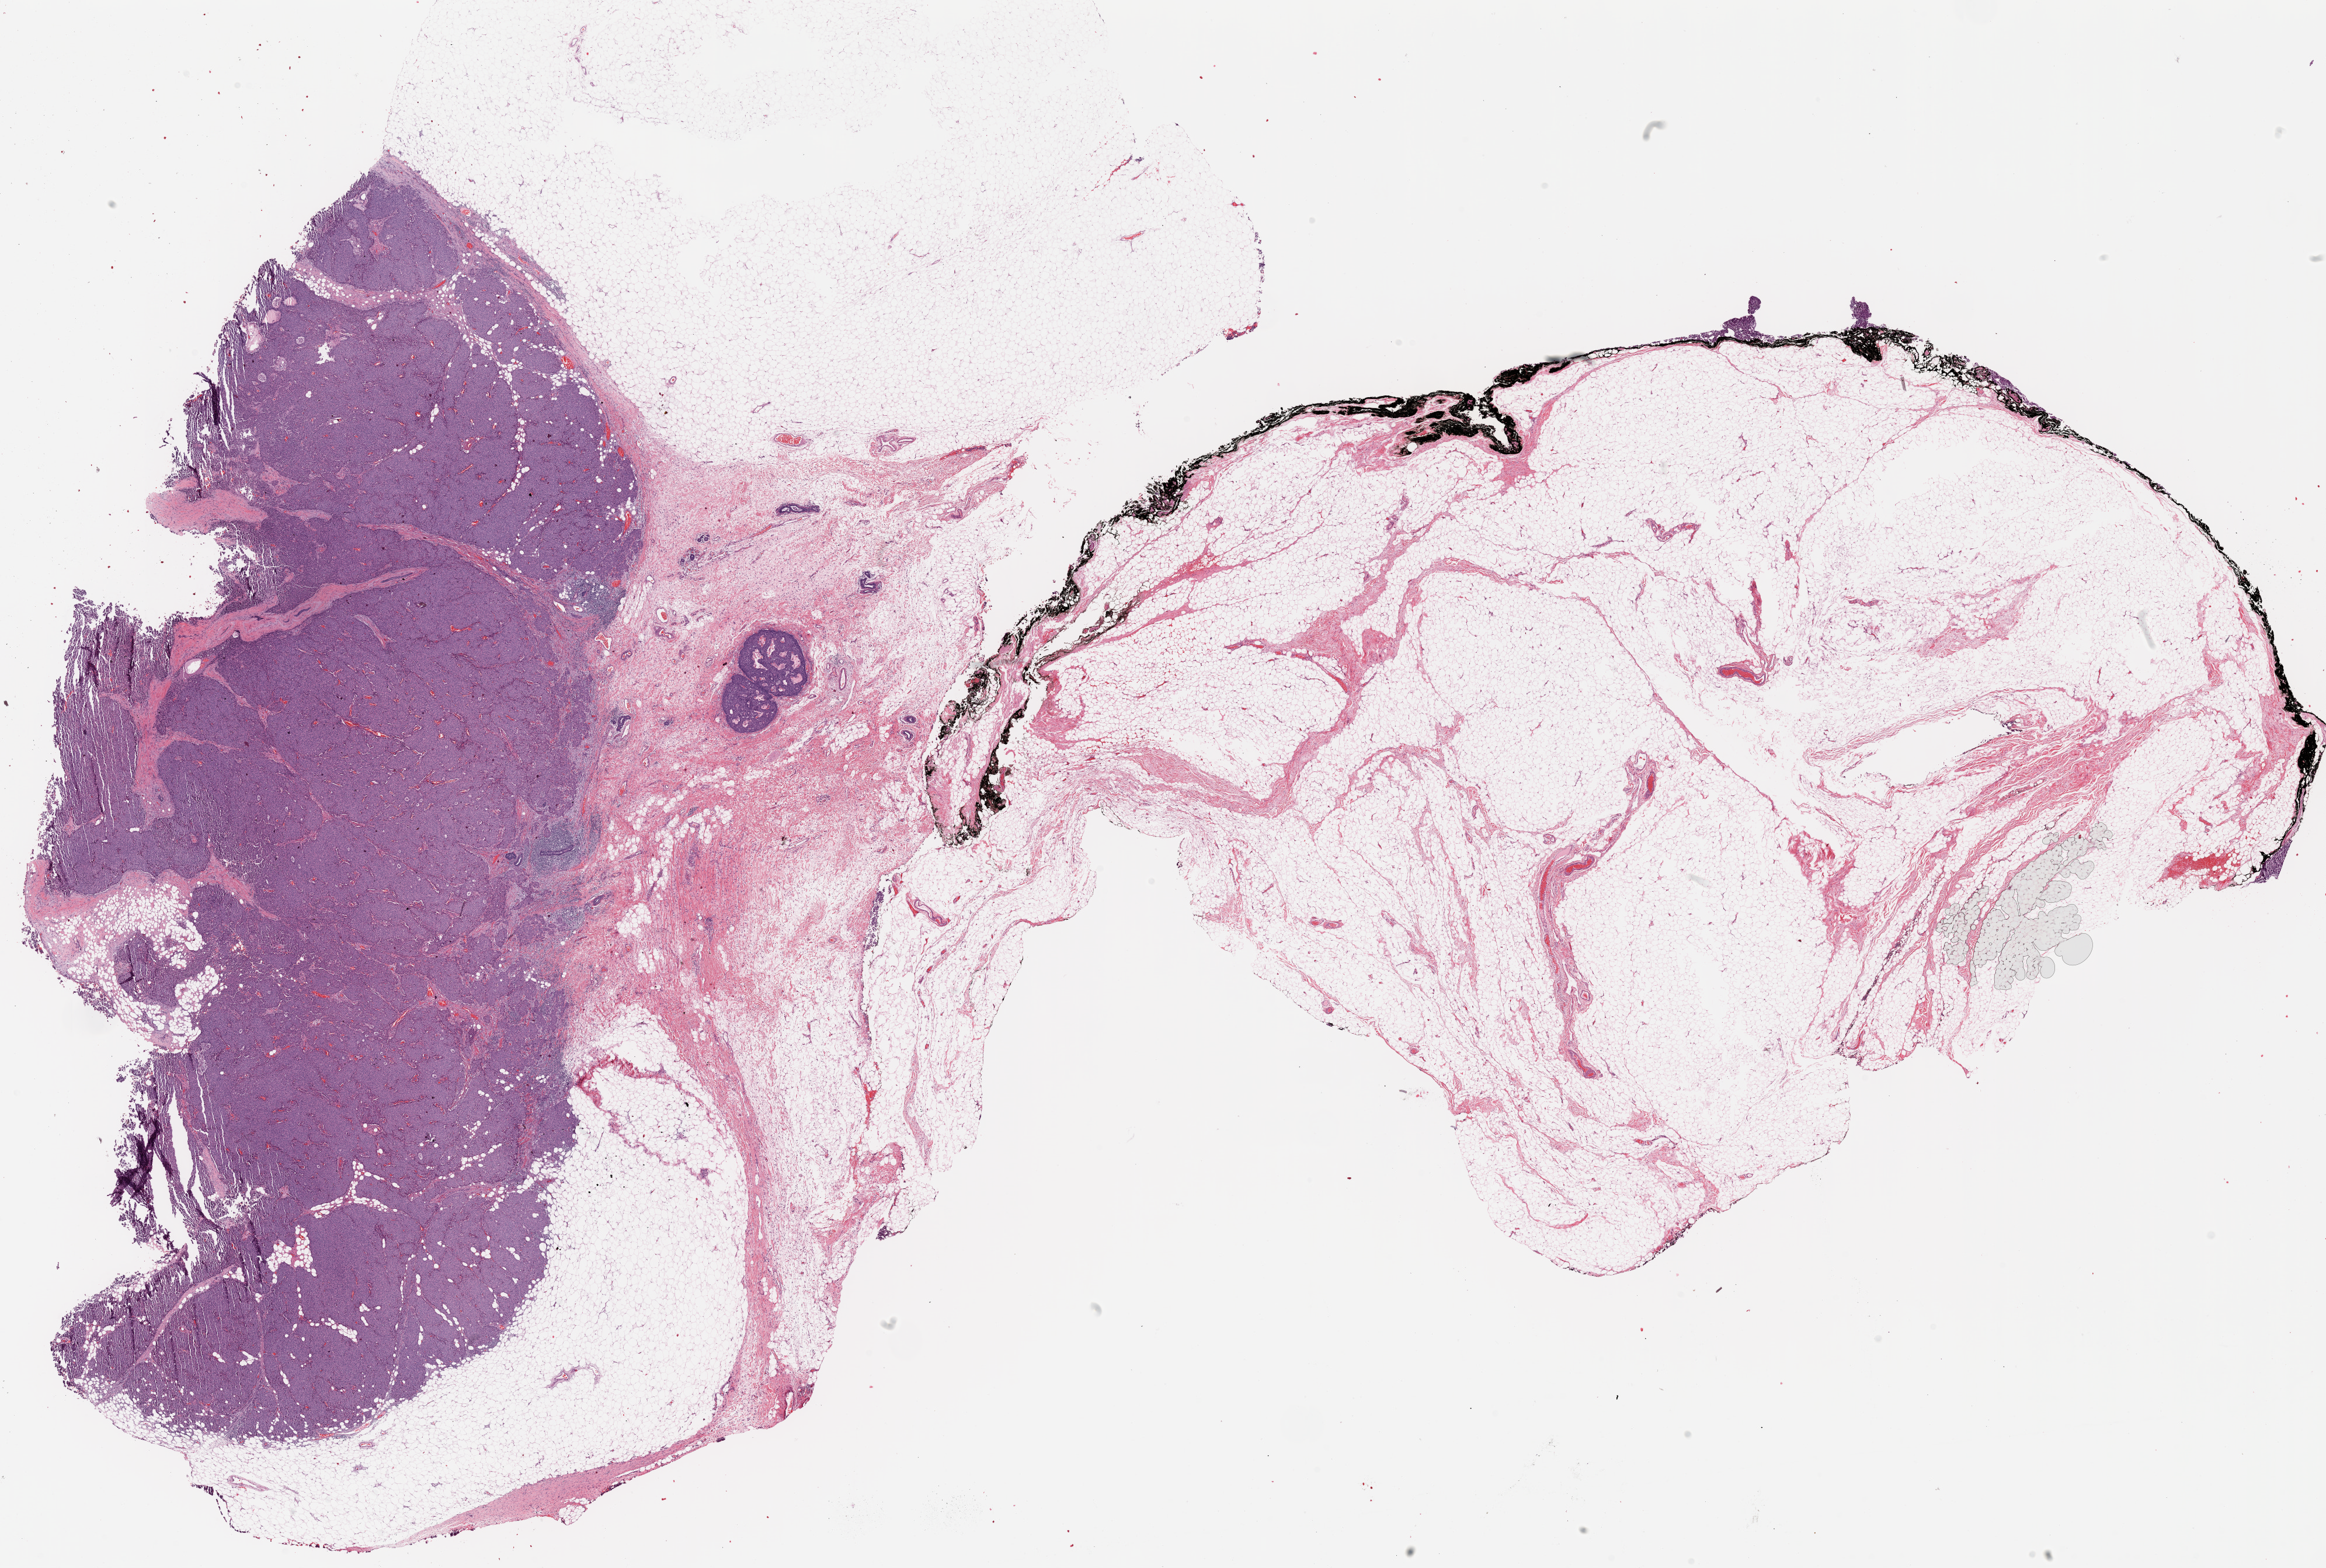
Digitized H&E tissue section (whole slide) — a low-resolution overview of the entire scanned area, about 31.8 x 21.5 mm (acquisition: 20x scan), formalin-fixed paraffin-embedded (FFPE) diagnostic section, breast, primary tumour sample. Female, age 63 years at initial diagnosis.
* lymph nodes positive (case pathology): 0 of 2 examined
* histologic diagnosis: Infiltrating duct carcinoma, NOS
* AJCC pathologic stage: IIA (6th edition)